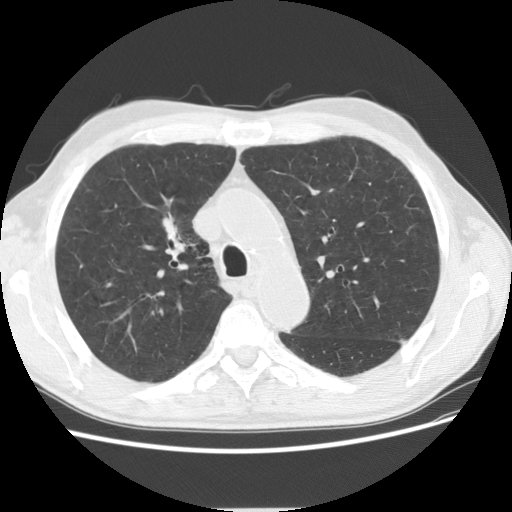
Axial slice from a low-dose chest CT screening exam; baseline screening round; lung window (W 1500 / L -600 HU); 2.5 mm slice thickness; standard (soft-tissue) reconstruction kernel (STANDARD); 120 kVp. Male participant, aged 73 years at enrolment.
Lesion marked by an expert reader, bounding box <142,202,205,261> (left, top, right, bottom; pixels). Screening reader's record for this exam (one nodule recorded; not confirmed to be the boxed lesion): non-calcified nodule or mass ≥4 mm, right upper lobe, 16 × 9 mm, spiculated (stellate) margins, soft tissue attenuation. Later outcome: lung cancer diagnosed 734 days after this screen (after the third annual screen) — squamous cell carcinoma, NOS, right upper lobe, poorly differentiated (G3), stage IIIB (AJCC 6th edition), 56 mm at pathology.